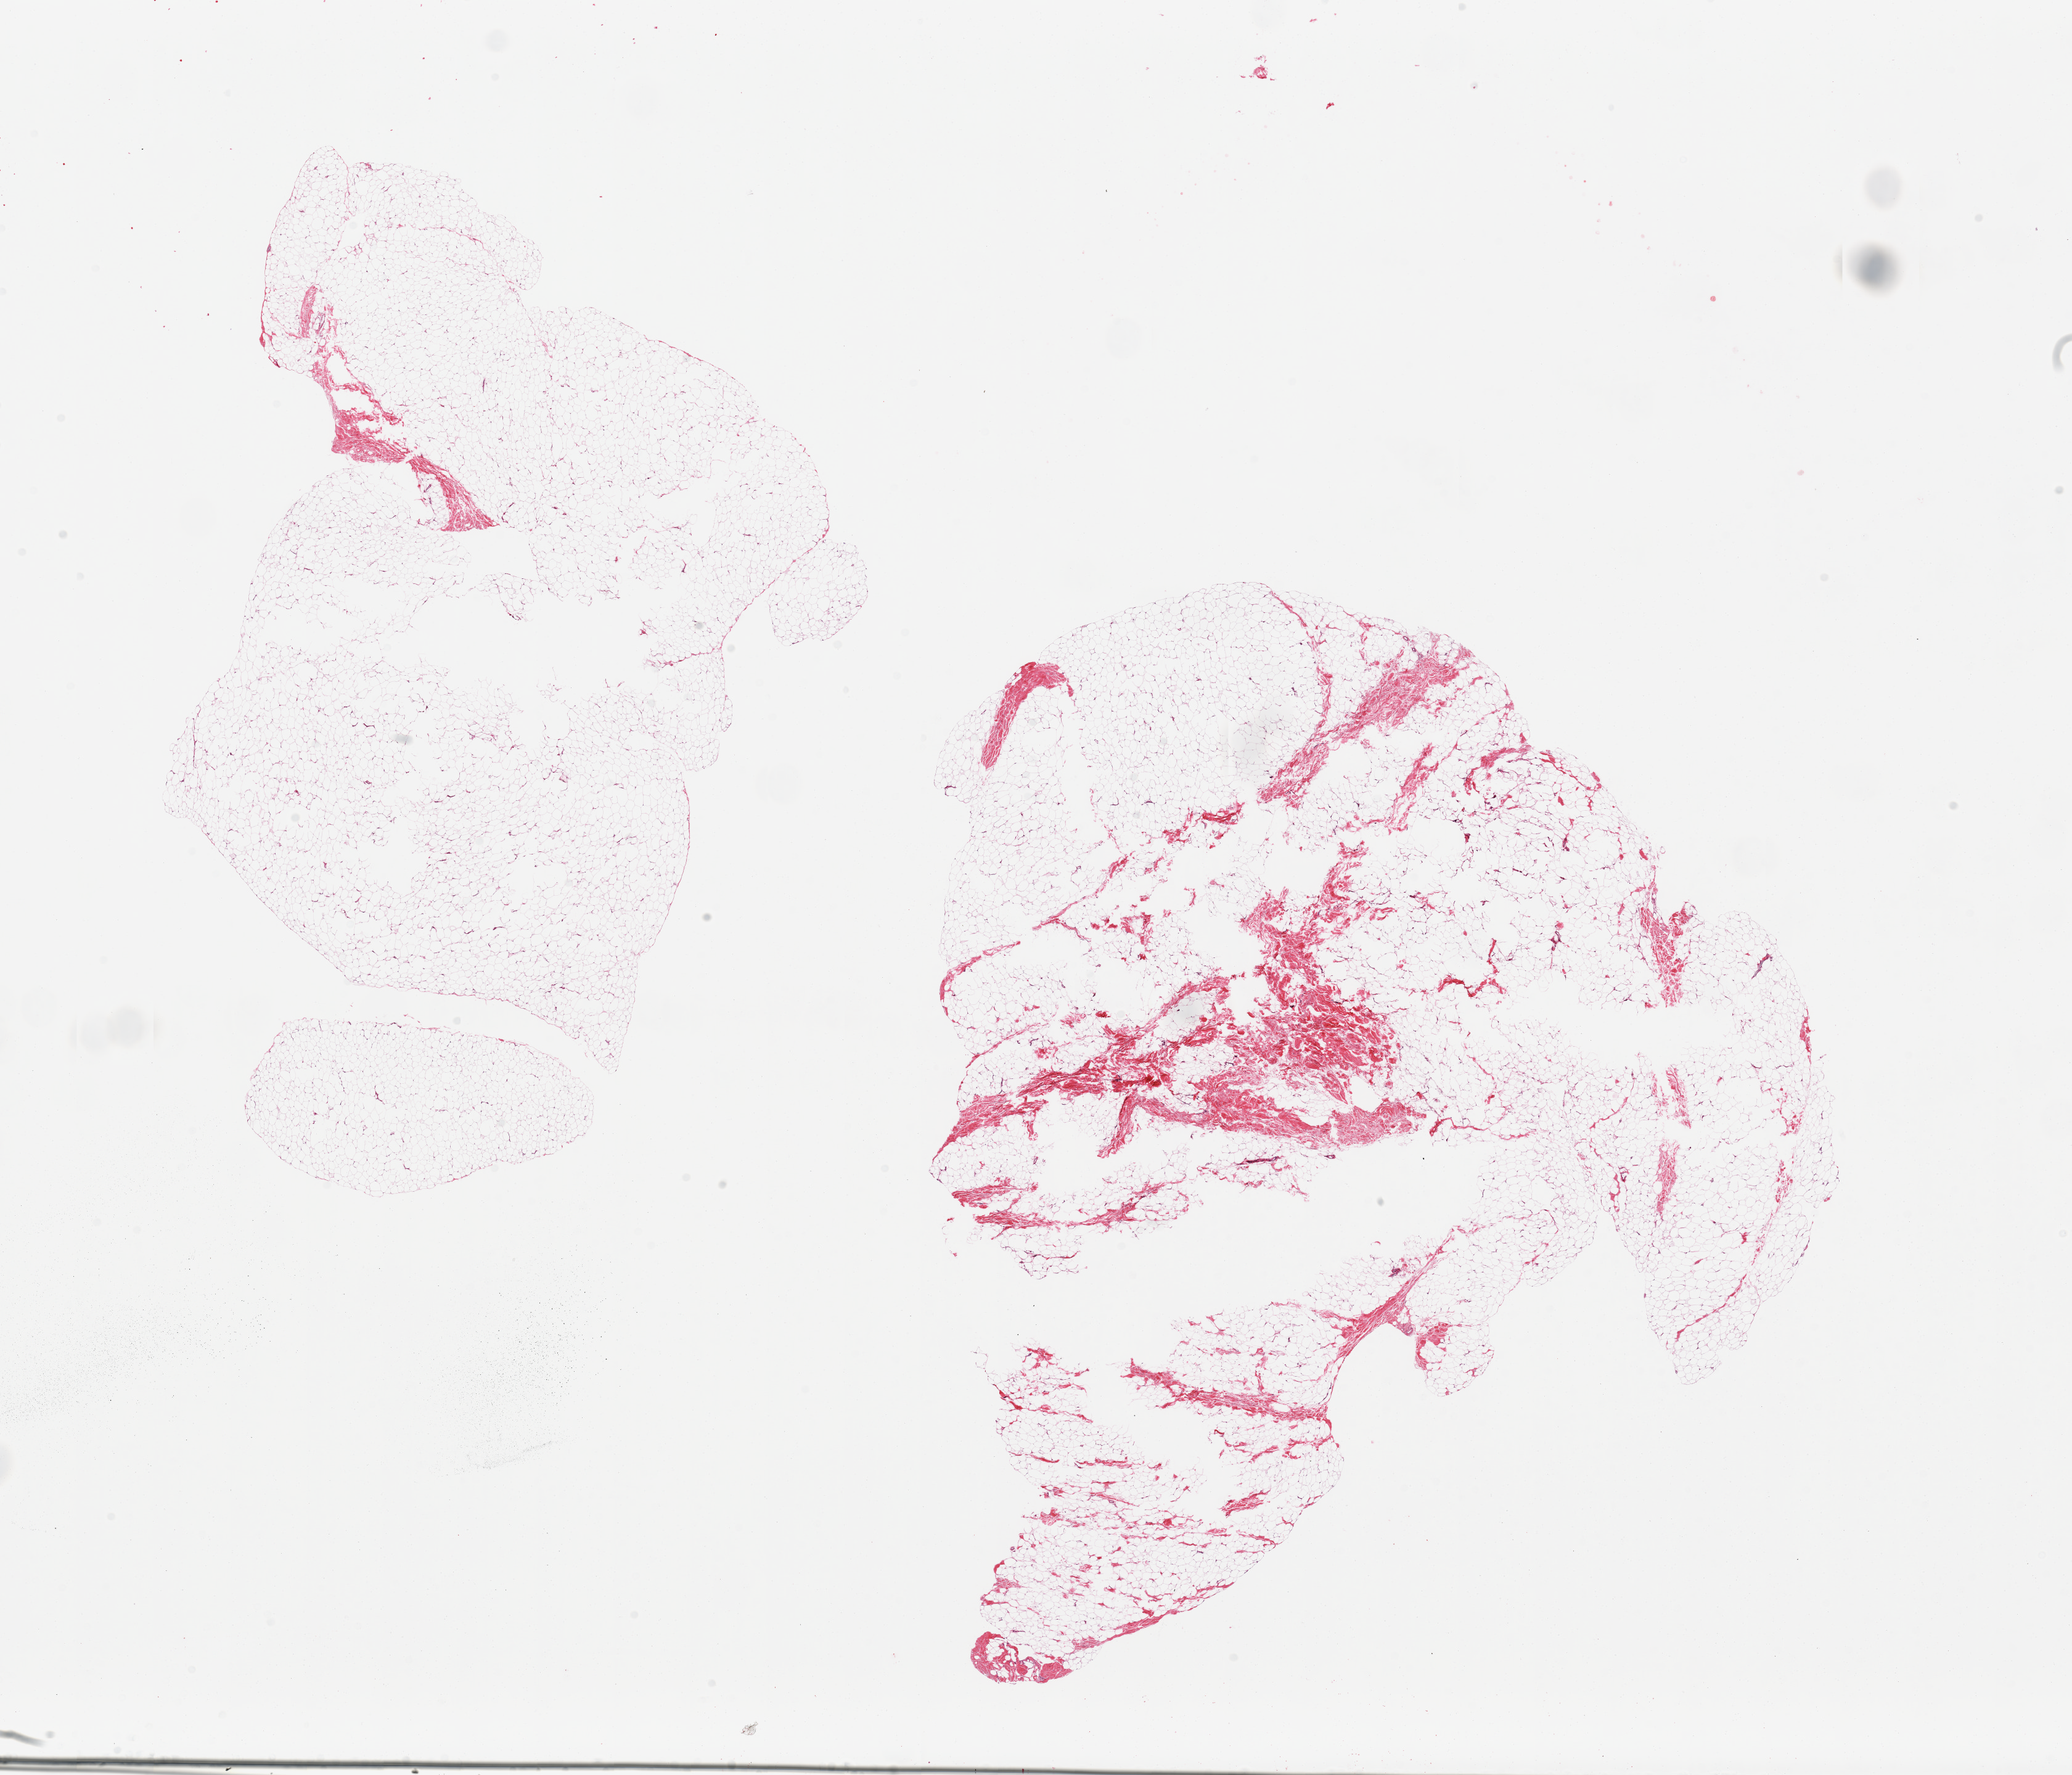
Haematoxylin and eosin whole-slide image, whole scanned area (about 26.6 x 22.8 mm, acquisition: 20x scan) shown as a low-resolution overview, PAXgene-fixed, paraffin-embedded tissue, section of breast (target tissue), donor tissue sample. Donor: male.
Review note (as recorded): 2 pieces, fibroadipose tissue, no ductal elements noted.